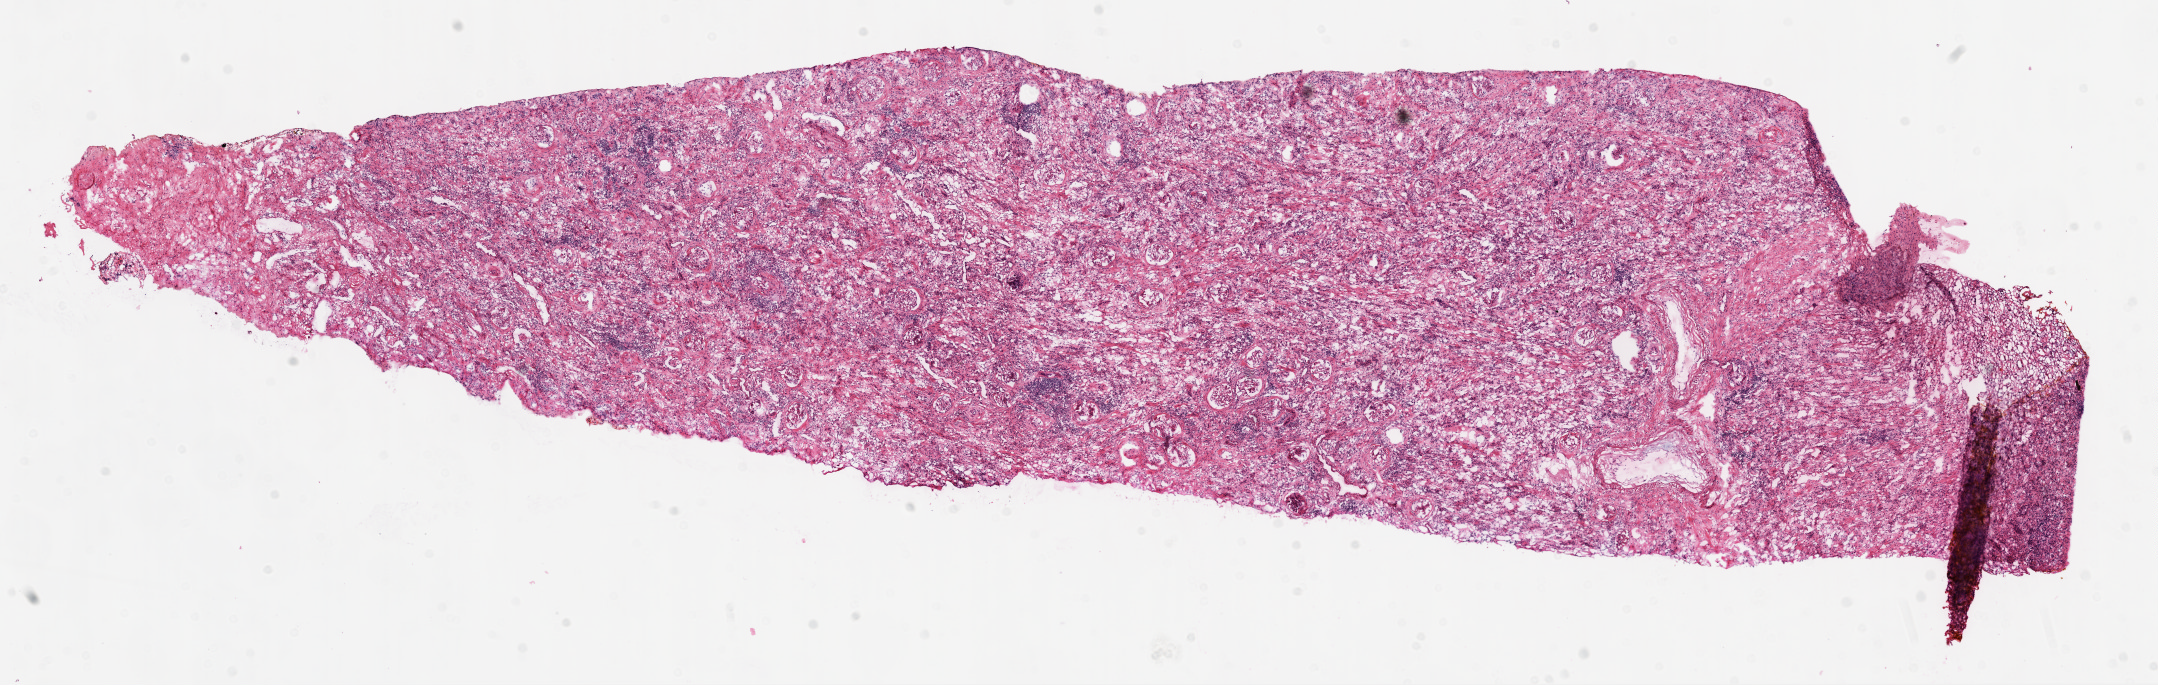
Digitized H&E tissue section (whole slide) — a low-resolution overview of the entire scanned area, about 17.4 x 5.5 mm. Frozen section from the top of the tissue portion. Kidney, solid tissue normal (non-tumour tissue) sample. Patient: male, age at initial diagnosis 61 years.
This section: solid tissue normal sample (biorepository sample class). Patient diagnosis: Clear cell adenocarcinoma, NOS.